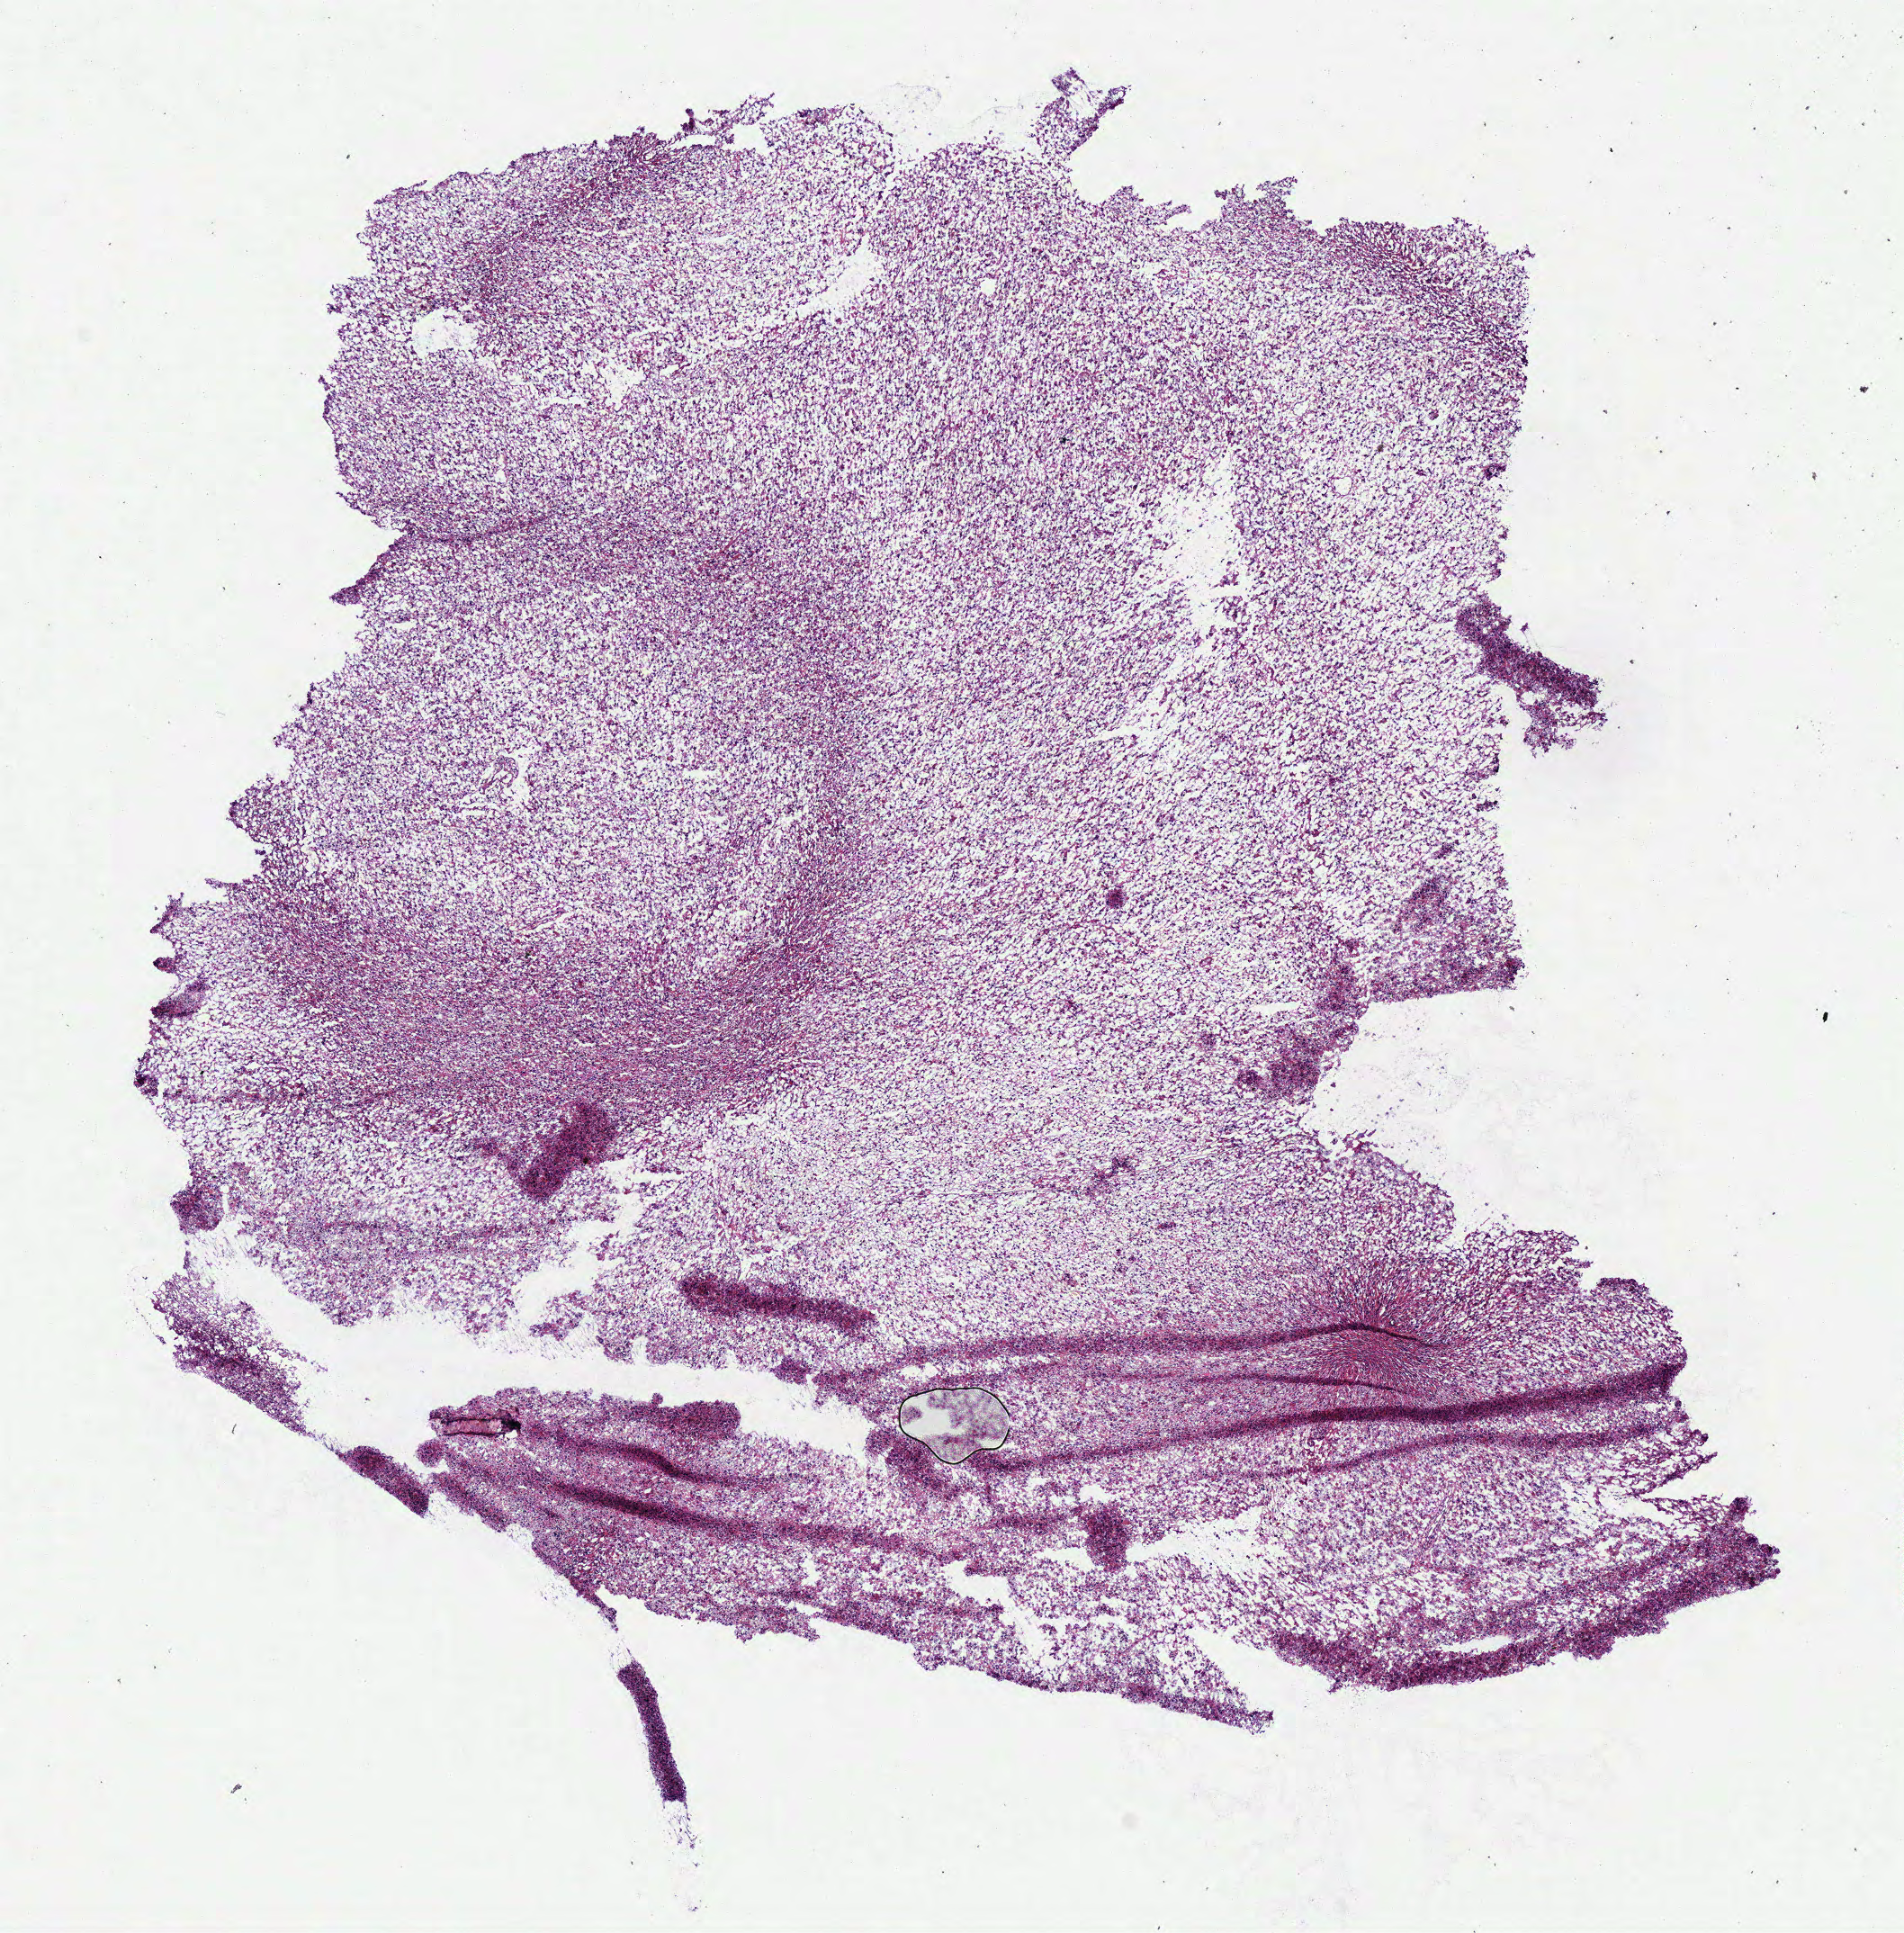
Digitized Hematoxylin and eosin (H&E) stained tissue section (whole slide) — shown as a low-resolution overview of the whole scanned area (about 8.3 x 8.4 mm); frozen section; sample: primary tumour, brain. Female, age 31 years at initial diagnosis. Histologic grade: G3 (poorly differentiated). Composition of this section per pathologist review: tumour cells 100%, tumour nuclei 80%, normal cells 0%, stromal cells 0%, necrosis 0%.
* pathologic diagnosis: Mixed glioma